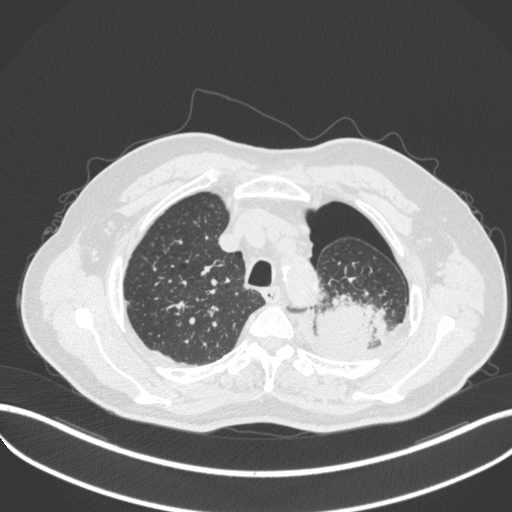
Chest CT, one axial slice. Position 404 of 466 along the scan axis. Reconstruction kernel B31f. 120 kVp. Lung window (W 1500 / L -600 HU). 1 mm slice thickness. 512 × 512 image matrix, field of view 400 × 400 mm. Male patient, age 76 years. From the clinical record (not read from this slice): clinical TNM (as recorded): T3 N0 M1b.
Annotated regions visible in this slice (rectangle marked by the reading radiologist):
- lung tumour (recorded histology: adenocarcinoma): bounding box [x1, y1, x2, y2] px = [307, 293, 391, 351]